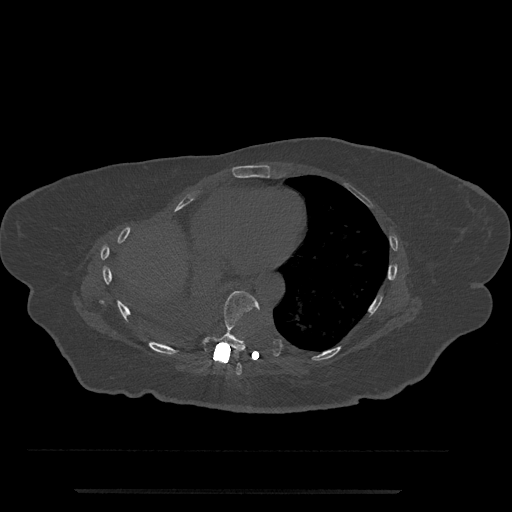
CT including the spine, one axial slice. Reconstruction kernel Br40s/3. 120 kVp. Bone window (W 1800 / L 400 HU). 0.5 mm slice thickness. 512 × 512 image matrix, field of view 440 × 440 mm. Patient: female, 51 years. From the clinical record (not read from this slice): primary cancer: neuro; vertebrae with lytic lesions (as recorded): T8.
Structures marked on this image (semi-automatic segmentation, software-assisted and operator-edited):
- T7 vertebra: bounding box (x1, y1, x2, y2) in pixels: (233, 363, 242, 376)
- T8 vertebra: (202, 291, 260, 351)